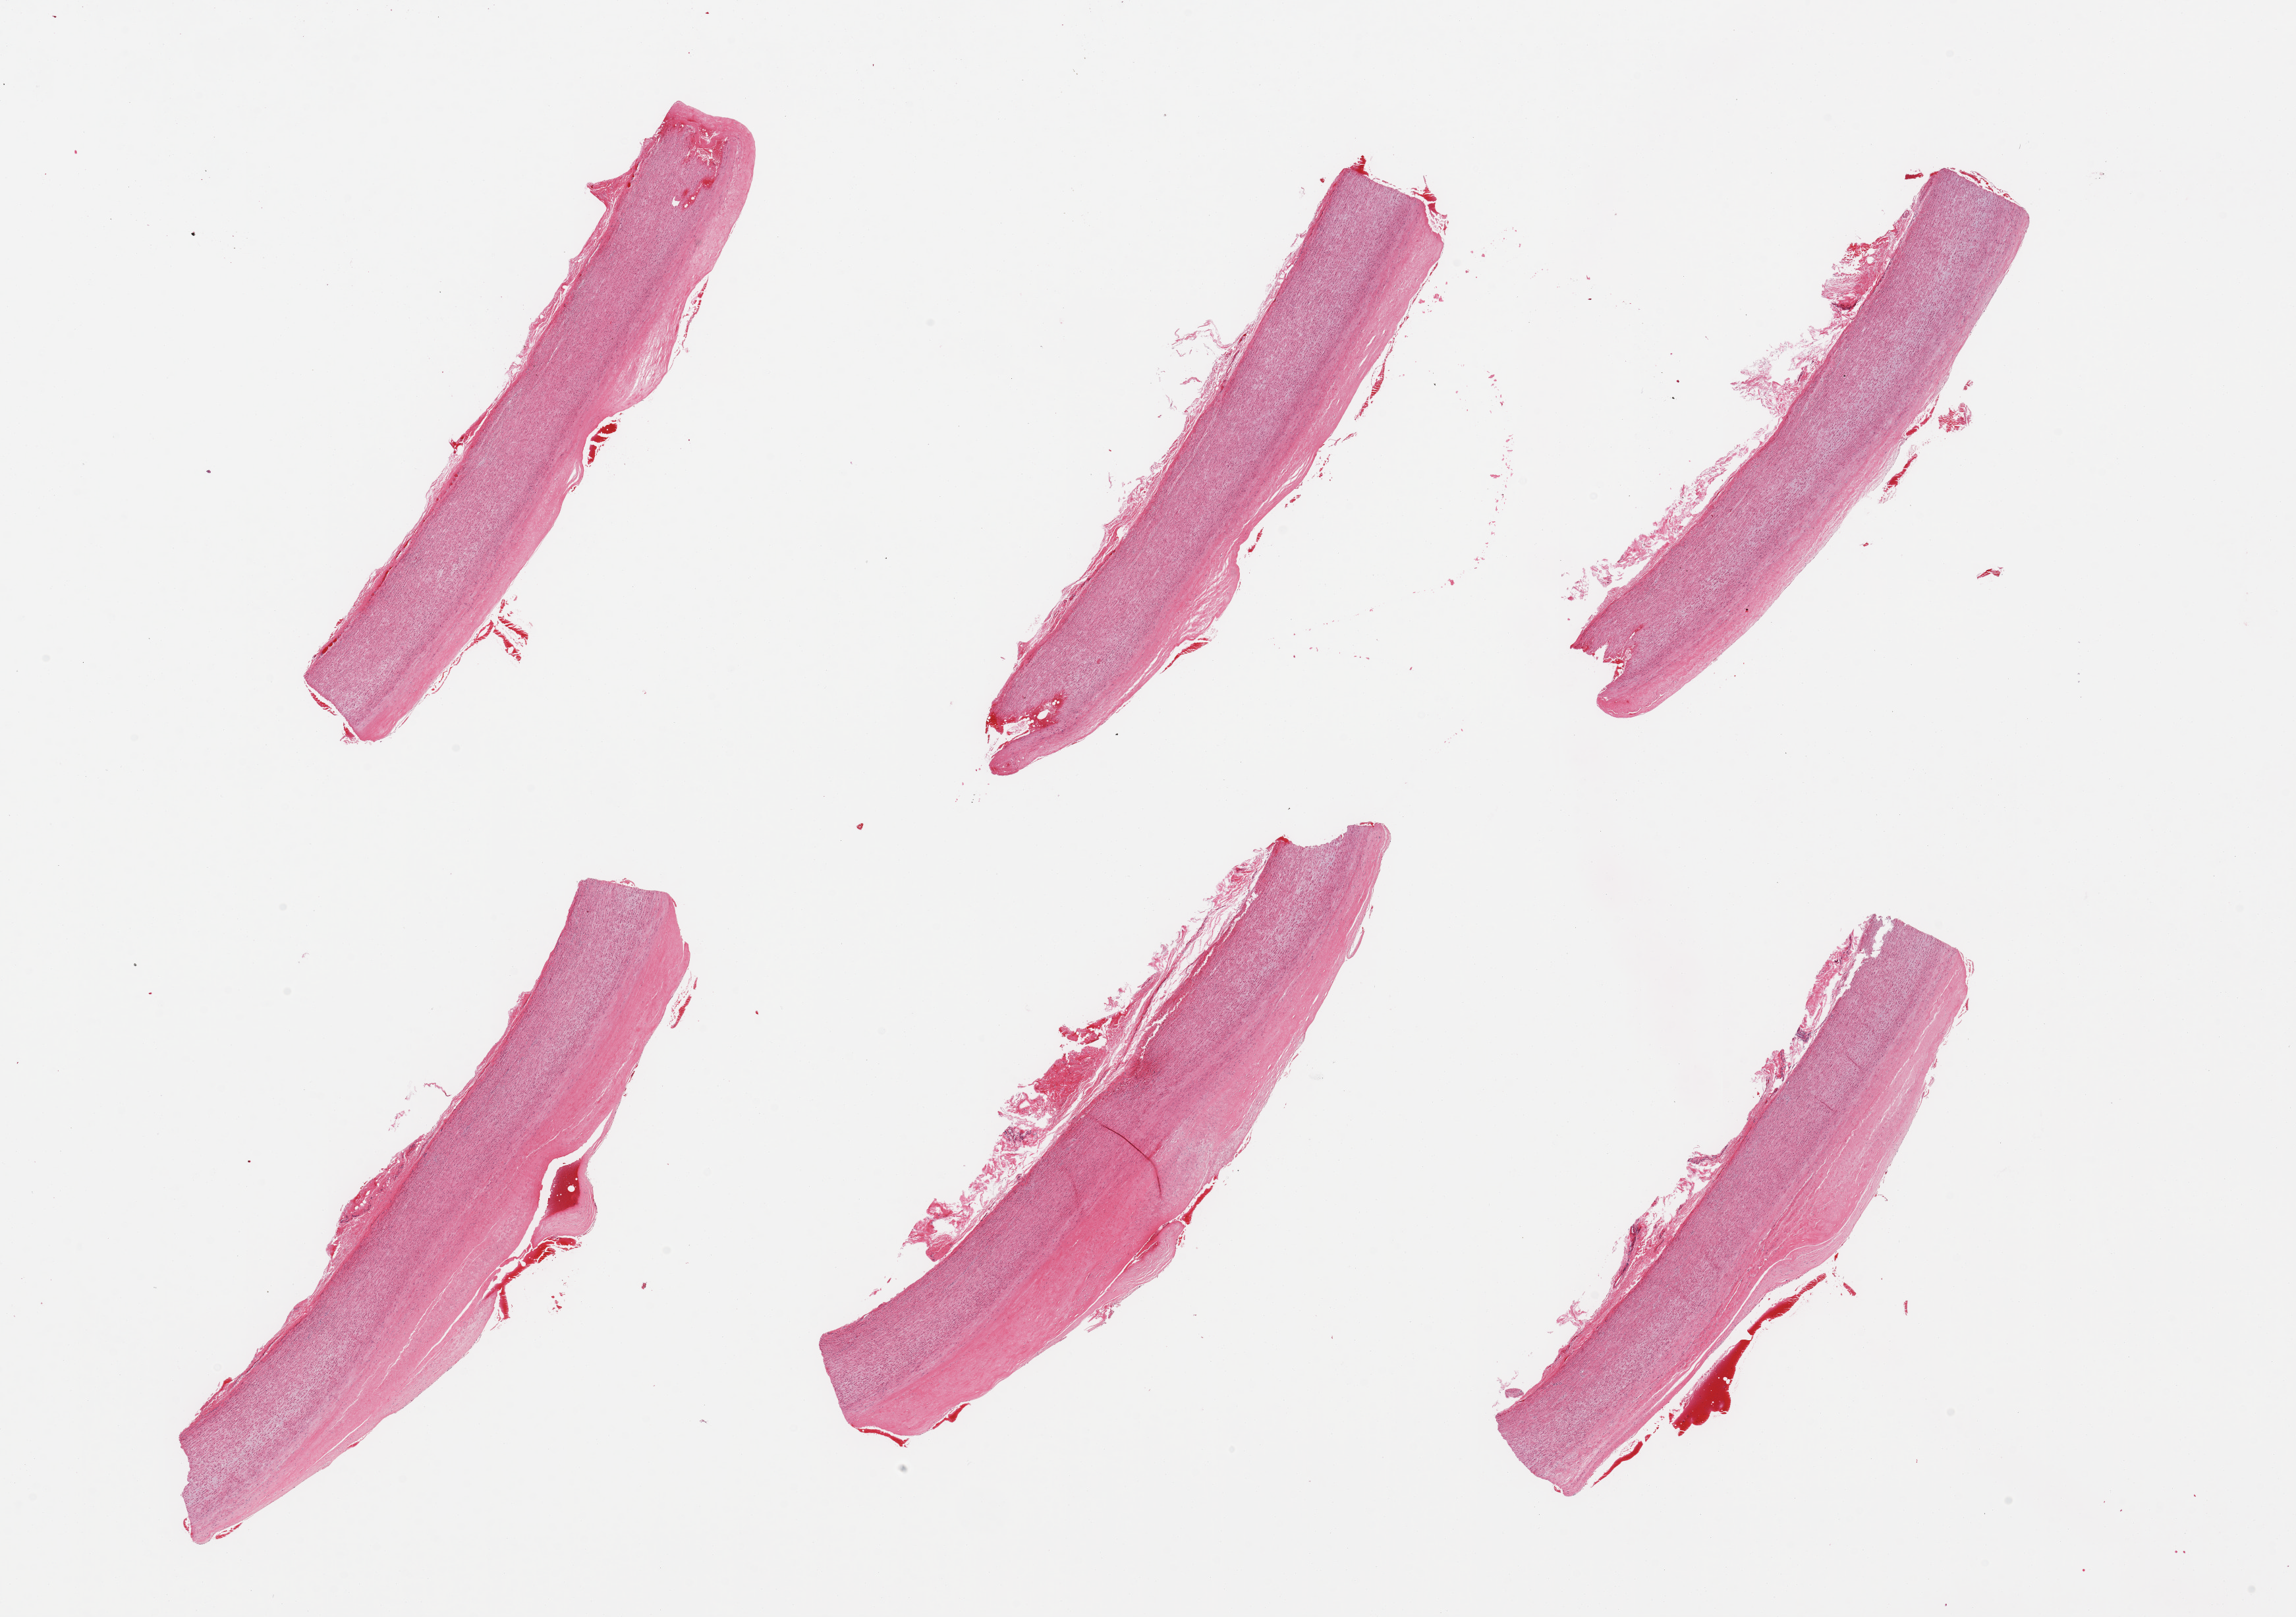
Whole-slide image, hematoxylin and eosin (H&E) stain, brightfield — low-resolution overview of the scanned area, about 27.6 x 19.4 mm; PAXgene-fixed paraffin-embedded (PFPE) section; sampled site (target tissue): aorta; tissue donor sample.
Pathologist's review note for this sample: 6 pieces; flatt plaques; small foci of dissecting hemorrhage in wall and plaque.